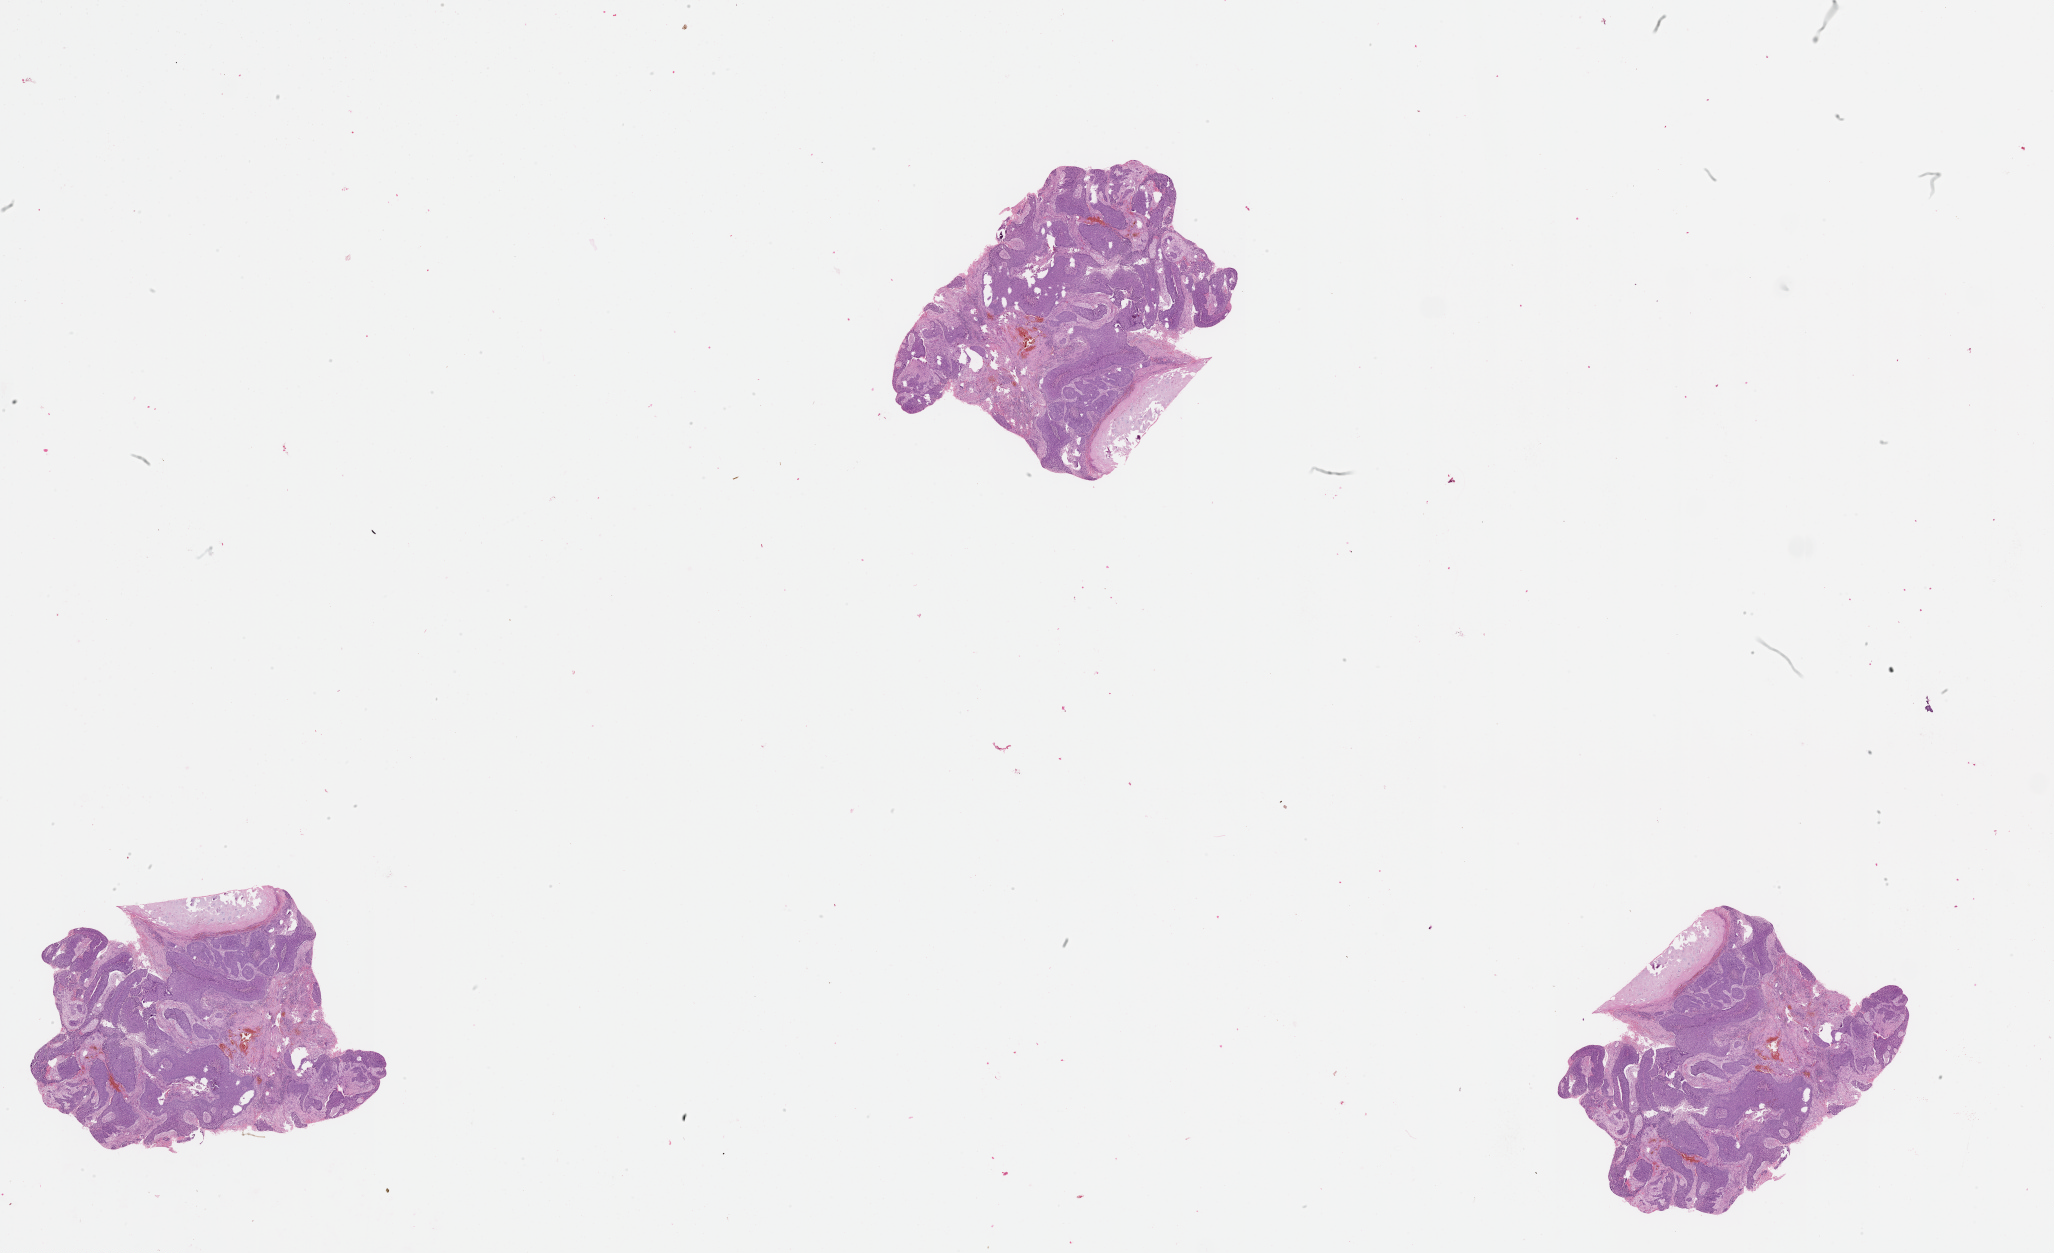
Hematoxylin and eosin (H&E) stained whole-slide image — low-resolution overview of the scanned area, about 33.1 x 20.2 mm, lung, tumour tissue. Male, 59 y/o.
Patient diagnosis (cohort enrolment): squamous cell carcinoma (lung).